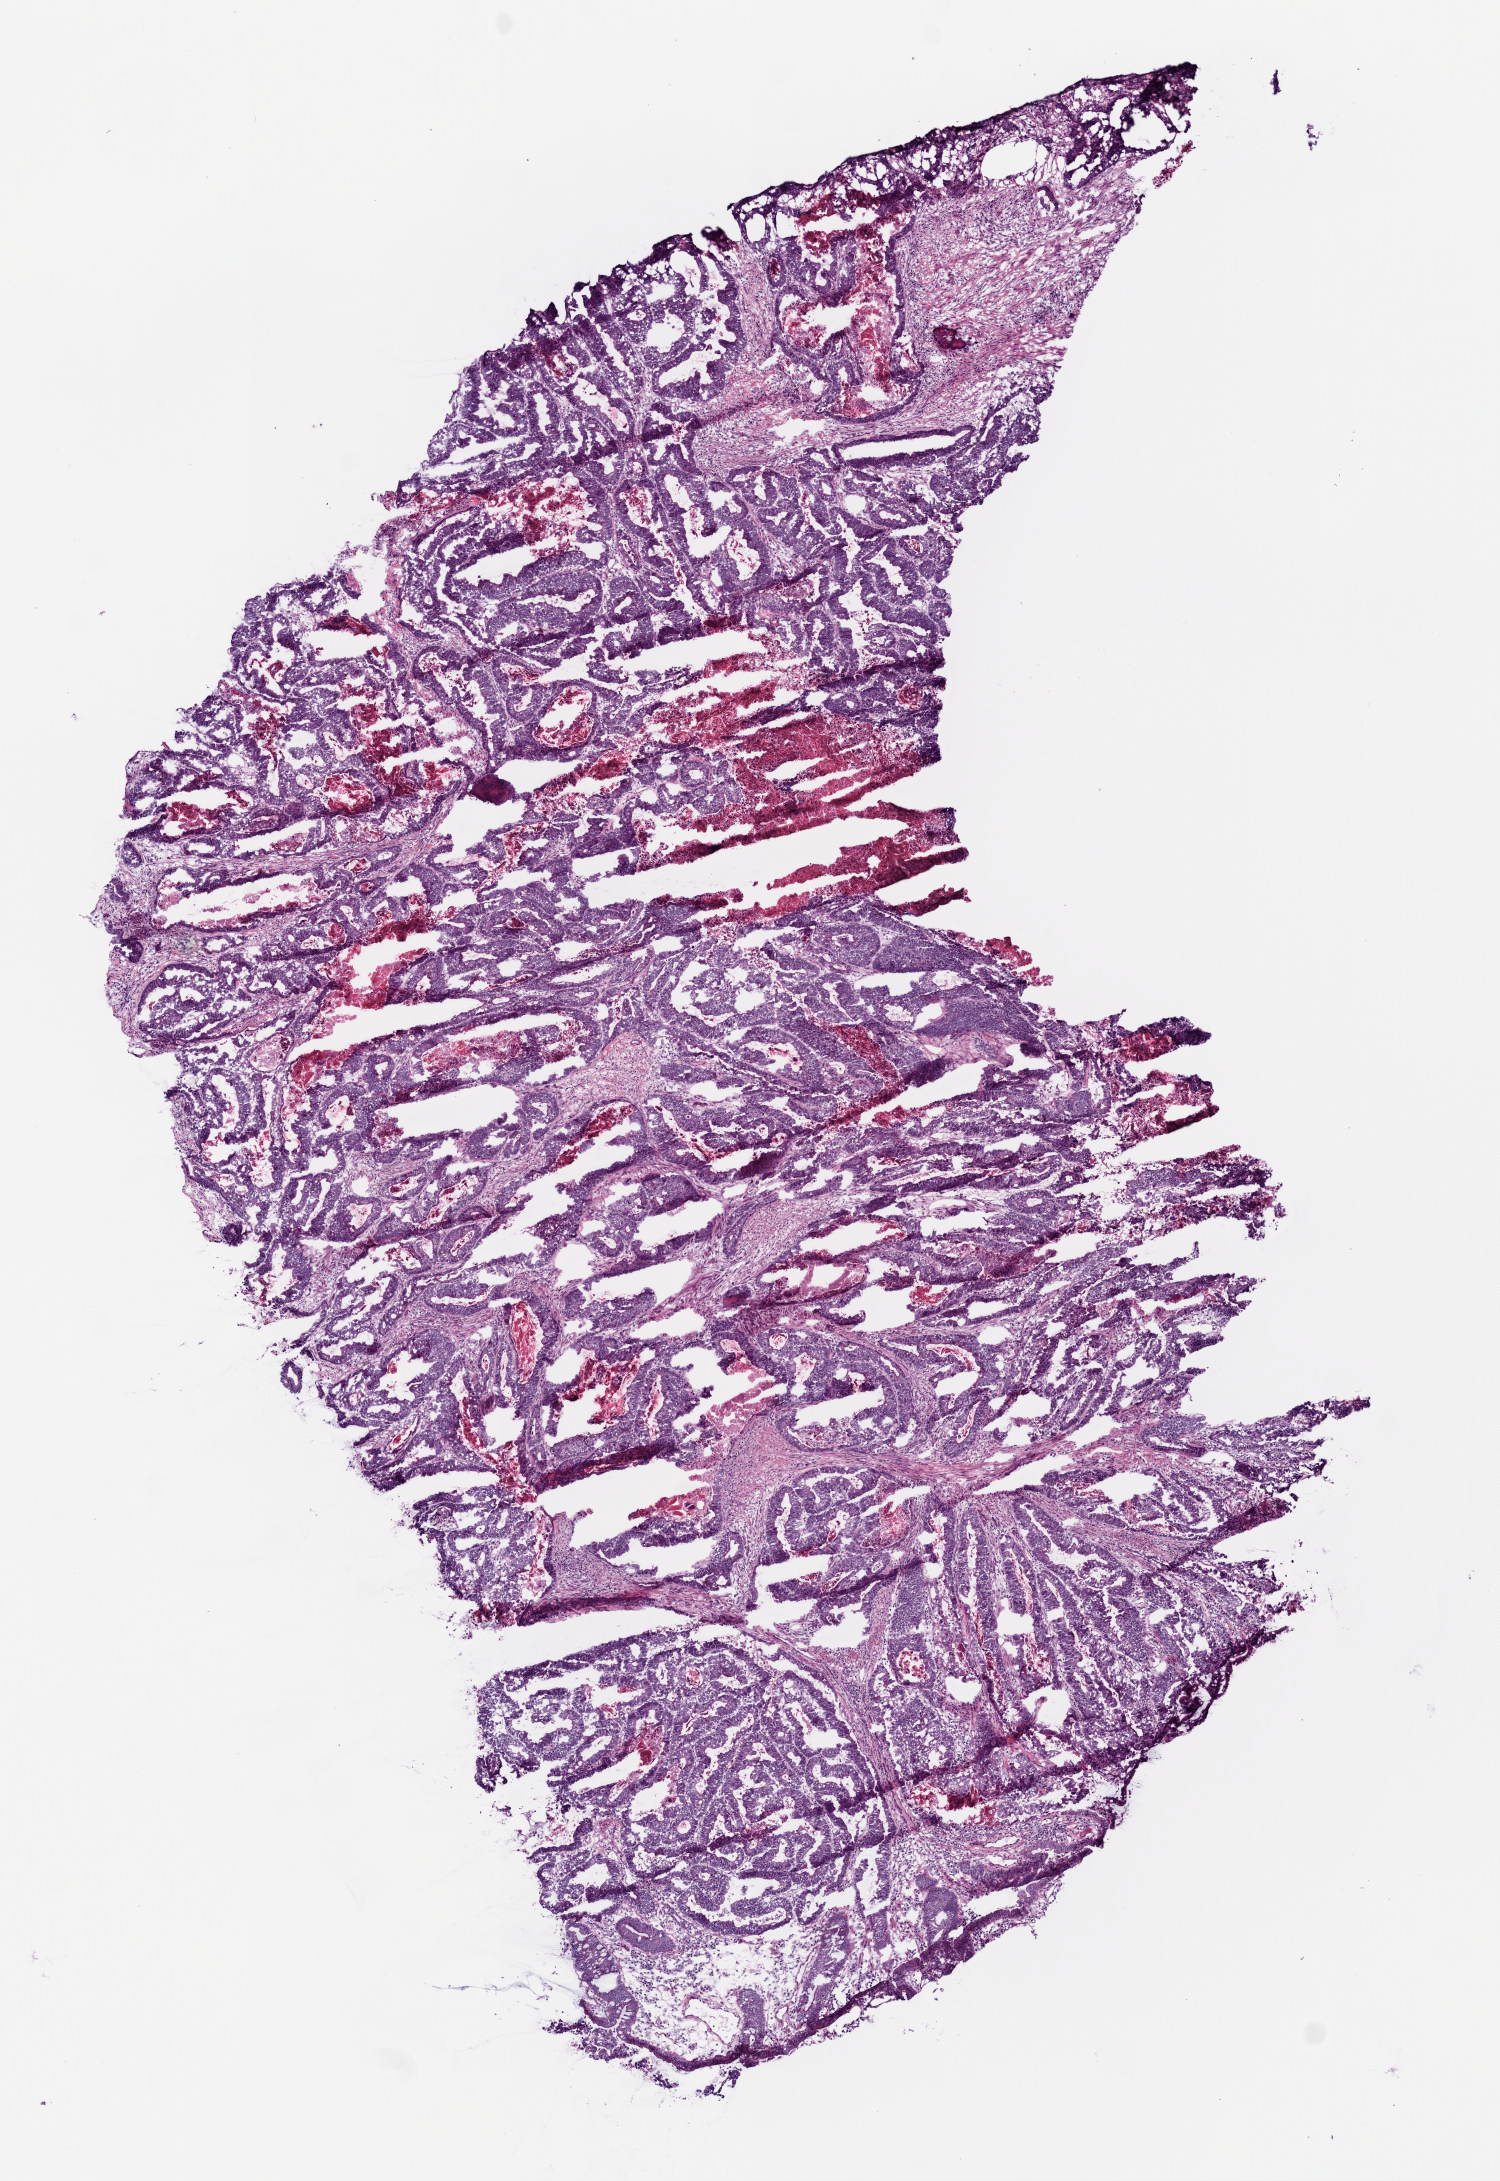
Hematoxylin and eosin (H&E) stained whole-slide image — whole scanned area (about 6.0 x 8.8 mm, acquisition: 20x scan) shown as a low-resolution overview; frozen section; sample: primary tumour, rectum. Female, age 65 years at initial diagnosis. Slide review estimates, as recorded: tumour cells 75%, tumour nuclei 91%, normal cells 0%, stromal cells 15%, necrosis 10%.
- diagnosis: Adenocarcinoma, NOS (rectosigmoid junction)
- TNM: T3 N2 M0
- AJCC pathologic stage: IIIC (6th edition)